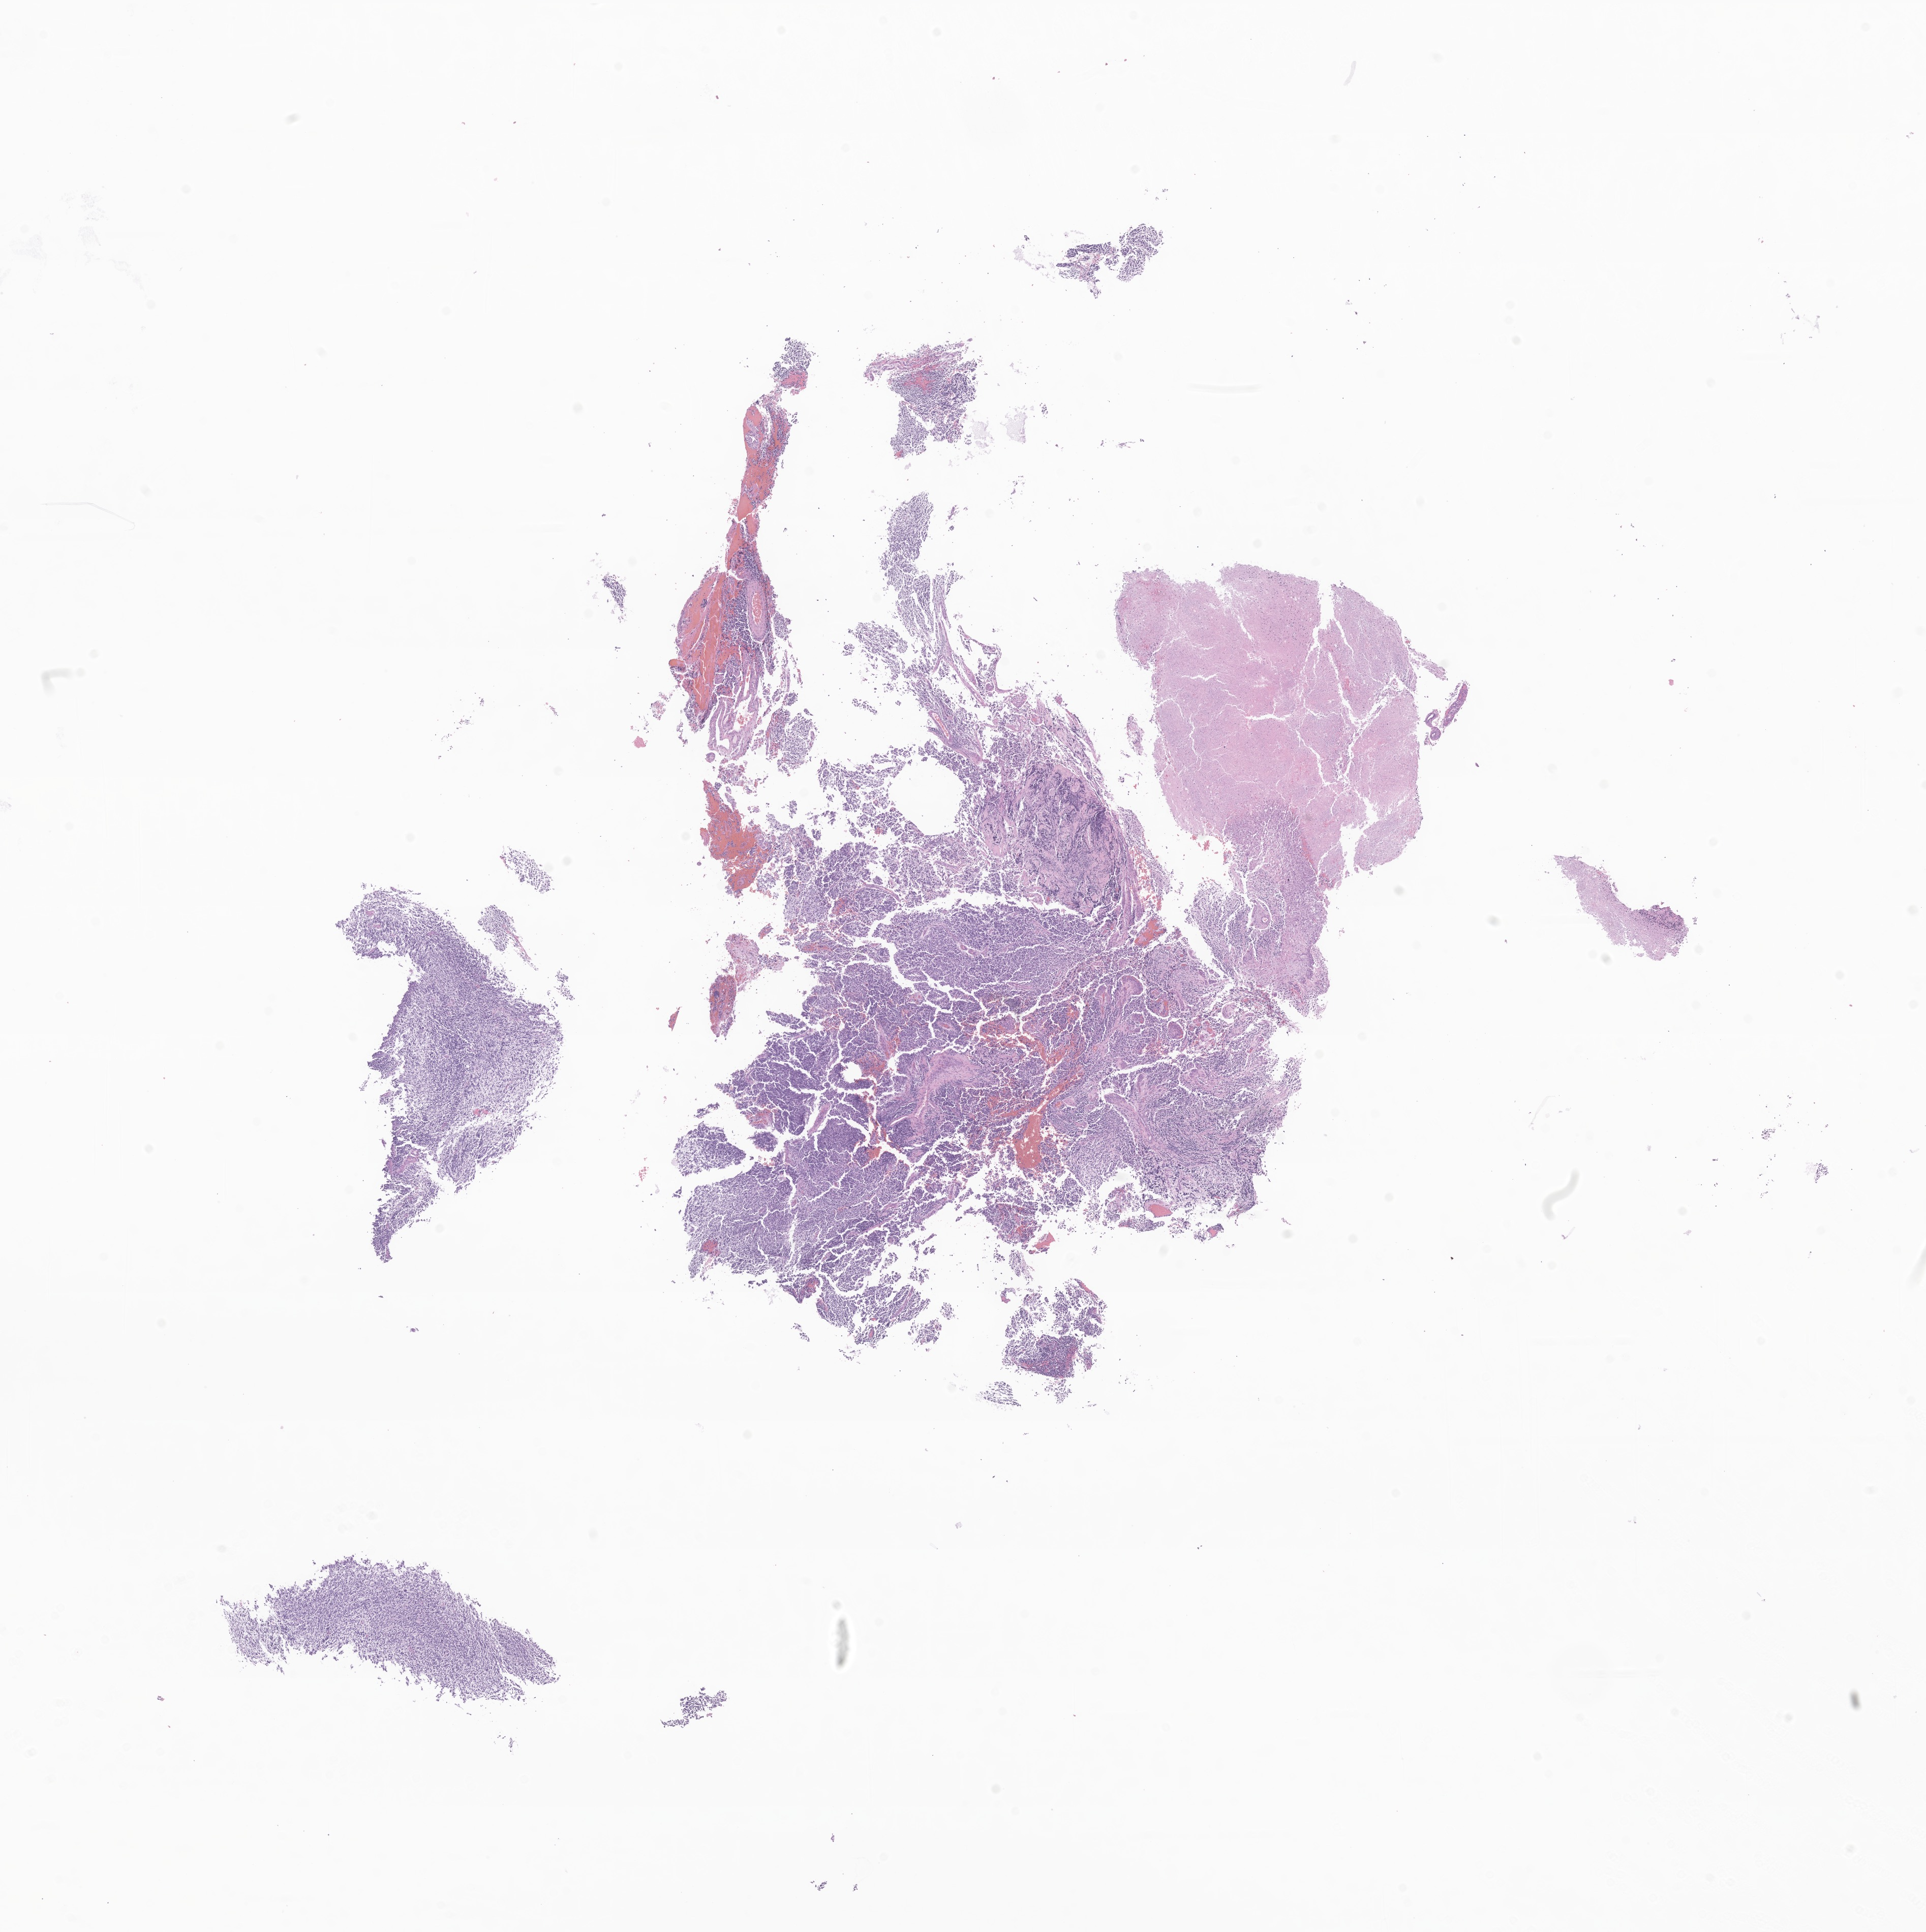
Haematoxylin and eosin whole-slide image of tumor tissue from the brain, whole scanned area (about 16.0 x 16.0 mm) shown as a low-resolution overview. Formalin-fixed, paraffin-embedded (FFPE) tissue. Patient: male, age 82 months (6 years 10 months).
Diagnosis: Medulloblastoma, NOS.